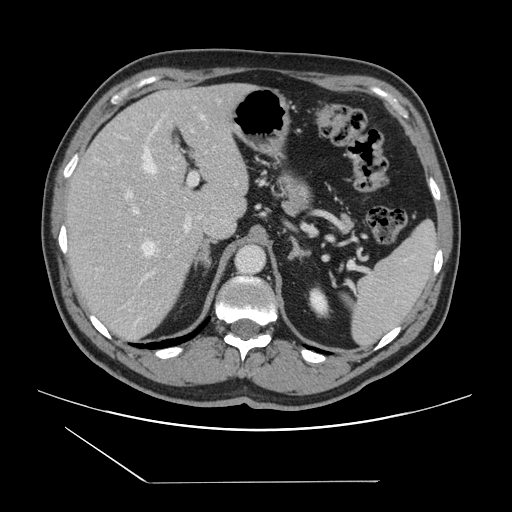
Contrast-enhanced abdominal CT, one axial slice; position 96 of 157 along the scan axis; 120 kVp; intravenous contrast given; soft-tissue window (W 400 / L 40 HU); 512 × 512 image matrix, field of view 407 × 407 mm. Male patient, age 61 years. Case-level facts recorded for this patient, not image findings: diagnosis: colorectal cancer liver metastases, imaged before liver resection; multiple liver metastases: yes; largest metastasis: 5.5 cm; chemotherapy before resection: no.
Annotated regions visible in this slice (outlined manually by an expert reader):
- hepatic veins: bounding box <142,115,205,255> (left, top, right, bottom; pixels)
- liver: <65,85,249,341>
- planned liver remnant (the part of the liver to remain after resection): <68,85,238,223>
- portal vein (with intrahepatic branches): <126,172,201,279>